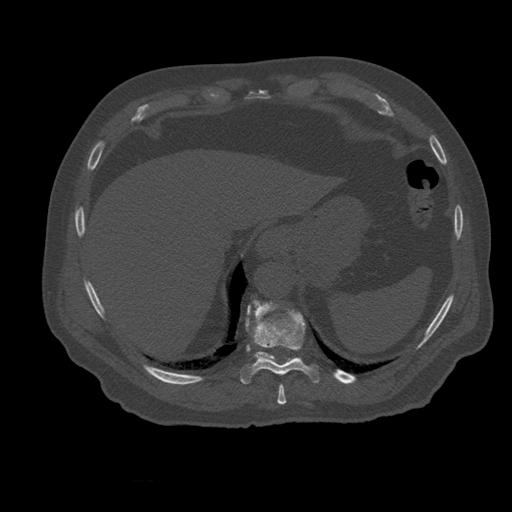
CT including the spine, one axial slice. Slice 300 of 399 in the series (ordered by position). Reconstruction kernel STANDARD. Bone window (W 1800 / L 400 HU). 1.25 mm slice thickness. 512 × 512 image matrix, field of view 407 × 407 mm. Patient age 73 years. From the clinical record (not read from this slice): primary cancer: prostate; vertebrae with lytic lesions (as recorded): L2.
Outlined on this slice (semi-automatically segmented with operator editing):
- T10 vertebra: bounding box [x1, y1, x2, y2] px = [241, 304, 320, 385]
- T11 vertebra: [246, 301, 276, 363]
- T9 vertebra: [278, 385, 287, 405]